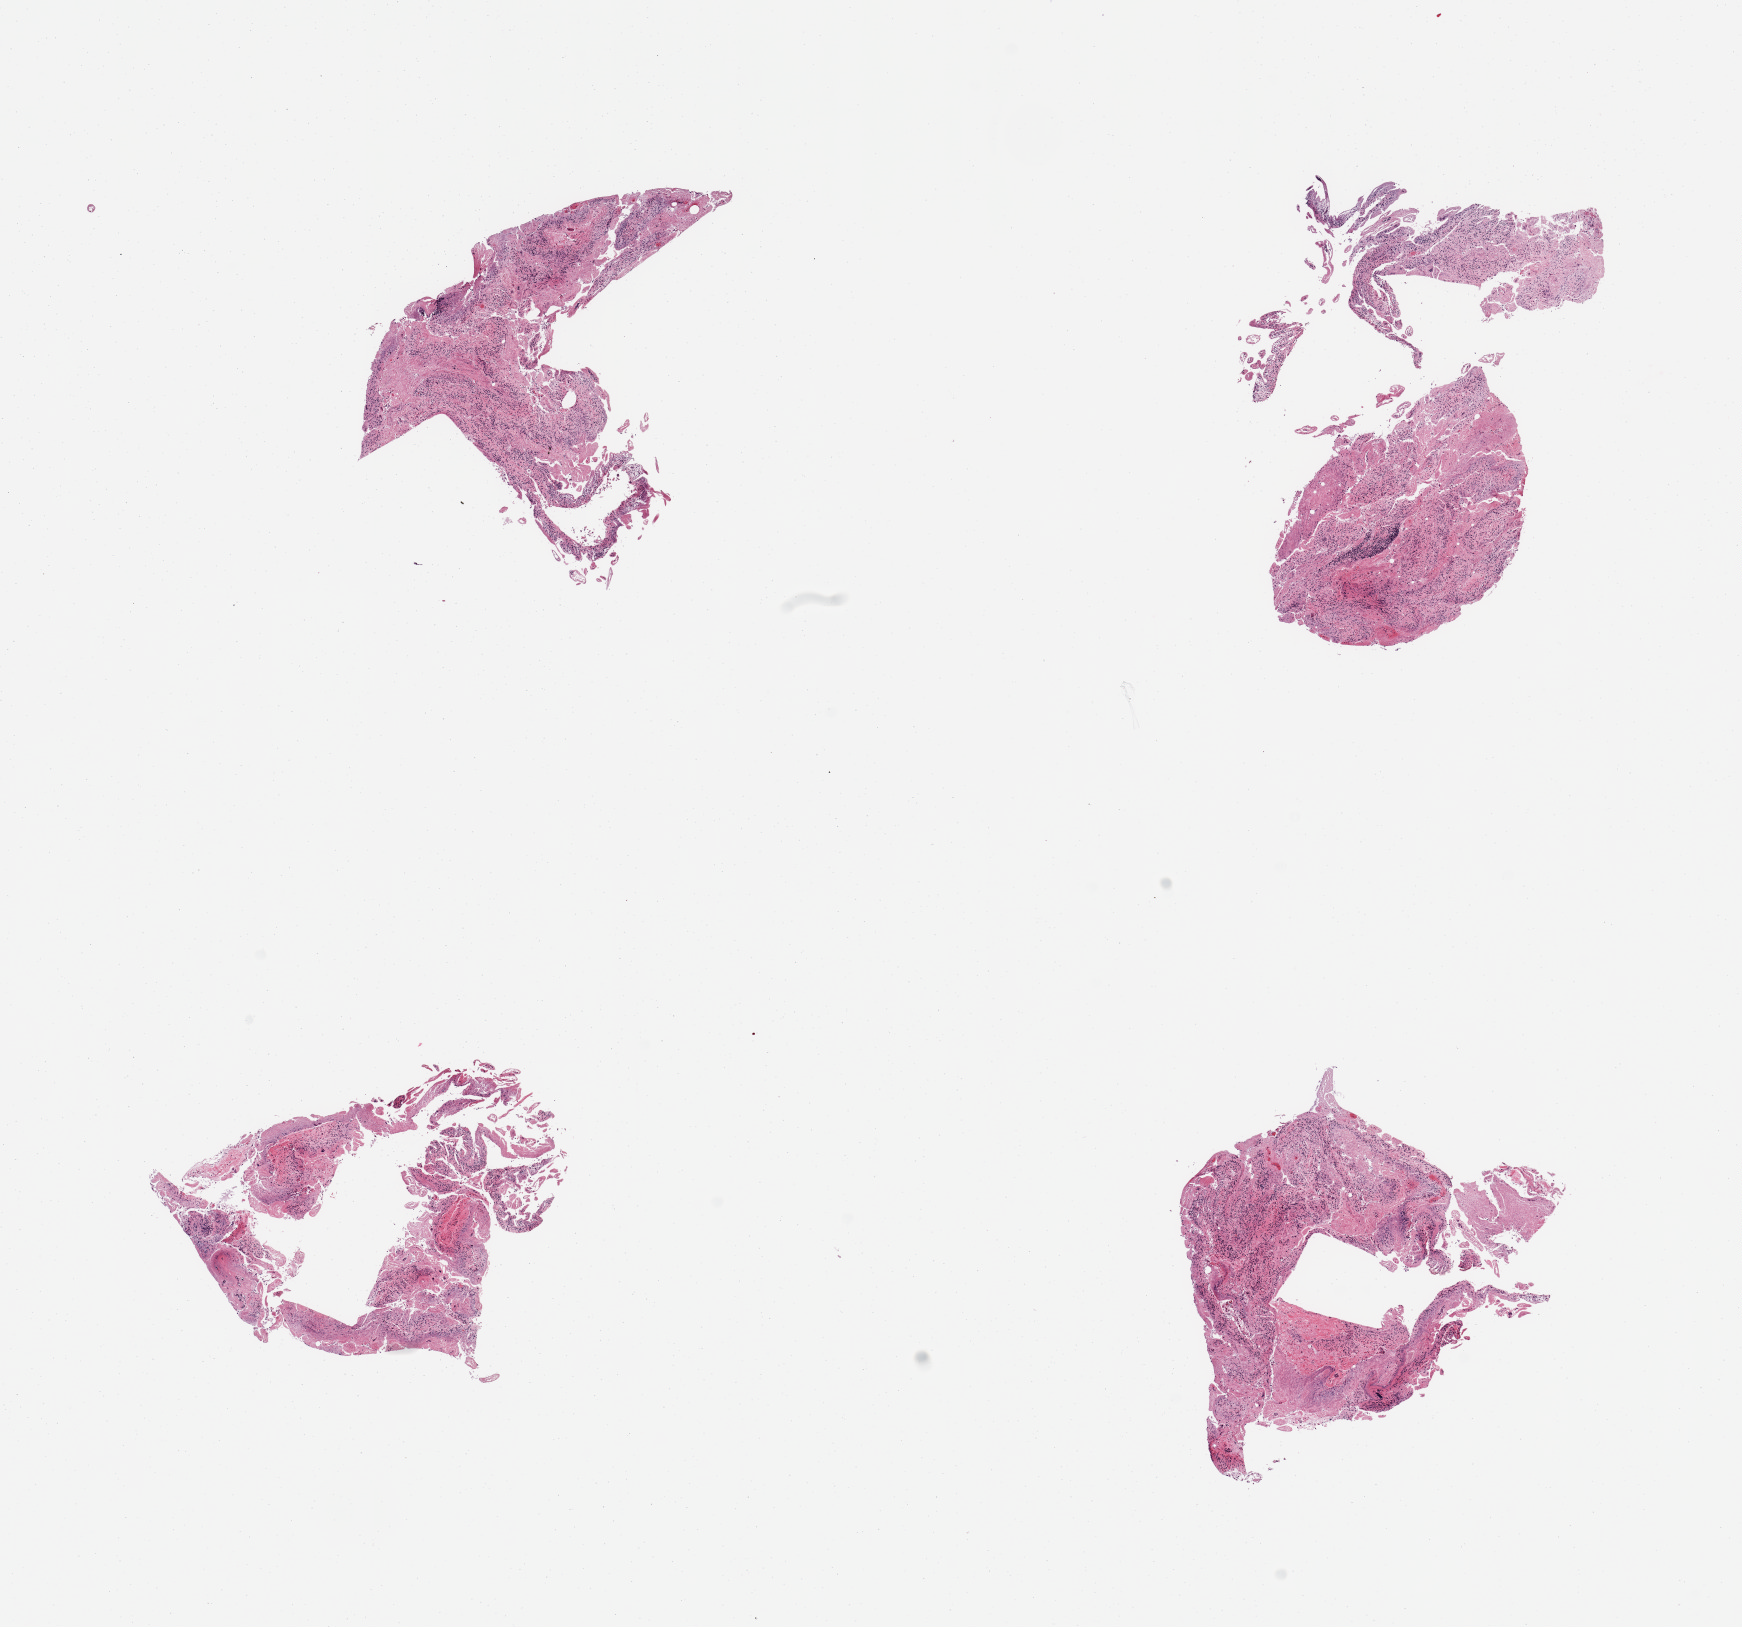
Digitized H&E-stained section, brightfield, a low-resolution overview of the entire scanned area, about 13.8 x 12.9 mm. PAXgene-fixed, paraffin-embedded tissue. Target tissue: ileum. Donor tissue sample. Female donor.
• pathologist's review note for this sample: 4 pieces; autolyzed mucosa & submucosa without significant lymphoid content